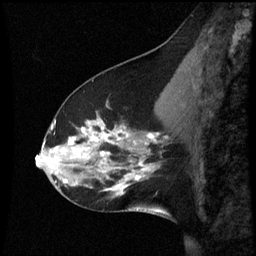
Breast MRI (dynamic contrast-enhanced), one sagittal slice. Dynamic contrast-enhanced series, image 2 of 3 at this slice position (ordered by acquisition). 1.5 T. TE 4.2 ms, TR 8.9 ms. 2 mm slice thickness. 256 × 256 image matrix, field of view 200 × 200 mm. Patient: female, 45 years. From the clinical record (not read from this slice): setting: breast cancer imaged before/during neoadjuvant chemotherapy; receptor status: HR-positive, HER2-negative.
Structures marked on this image (semi-automatically segmented with operator editing):
- analysis volume of interest (the breast-tissue region the enhancement analysis was run in; not a lesion): bounding box <46,94,171,205> (left, top, right, bottom; pixels)
- tumour enhancement mask (voxels above the 70 % enhancement threshold inside the analysis volume of interest): <46,124,167,183>